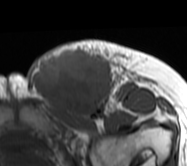
MRI of an extremity soft-tissue mass, one axial slice; position 34 of 62 along the scan axis; MR volume resampled by the dataset authors to the PET/CT grid (not the native acquisition matrix); 3.27 mm slice thickness; 187 × 166 image matrix, field of view 183 × 162 mm. Female patient. Case-level facts recorded for this patient, not image findings: histological type: leiomyosarcoma; grade: high; site of the primary tumour: groin.
Outlined on this slice (expert contour drawn on MRI and transferred to this co-registered scan by the dataset authors):
- gross tumour volume including surrounding oedema: bounding box (x1, y1, x2, y2) in pixels: (29, 39, 149, 120)
- gross tumour volume (mass): (30, 46, 115, 120)